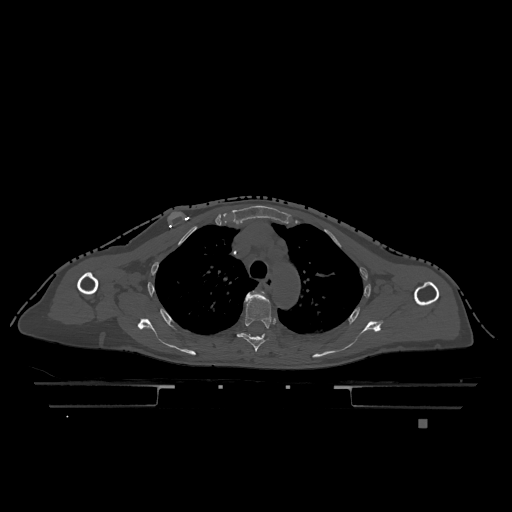
CT including the spine, one axial slice; slice 881 of 1317 in the series (ordered by position); bone window (W 1800 / L 400 HU); 0.5 mm slice thickness; 512 × 512 image matrix. Patient: female, 74 years. Case-level facts recorded for this patient, not image findings: primary cancer: lung; vertebrae with lytic lesions (as recorded): T1, T4, T5, T6, L4, L5.
Annotated regions visible in this slice (semi-automatically segmented with operator editing):
- T3 vertebra: box from (x=256, y=291) to (x=260, y=294) px
- T4 vertebra: (x=237, y=291)–(x=276, y=352)